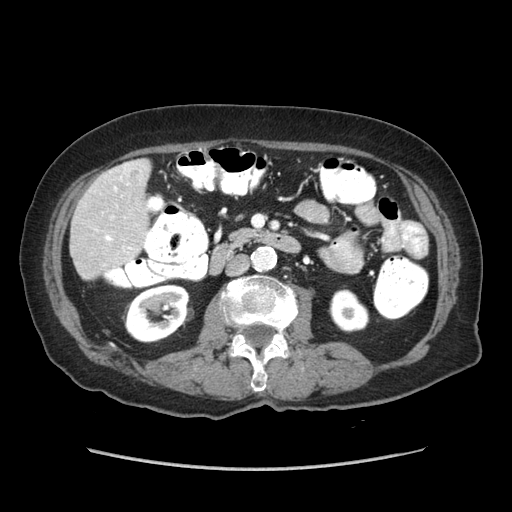
Contrast-enhanced abdominal CT (liver protocol), one axial slice; position 18 of 89 along the scan axis; reconstruction kernel STANDARD; soft-tissue window (W 400 / L 40 HU); 2.5 mm slice thickness; 512 × 512 image matrix, field of view 360 × 360 mm. From the clinical record (not read from this slice): diagnosis: hepatocellular carcinoma (patient treated with transarterial chemoembolisation; whether this scan precedes or follows treatment is not stated here); TNM stage (as recorded): Stage-IIIA; Child-Pugh class: A; tumour differentiation: well differentiated; tumour nodularity: multinodular.
Annotated regions visible in this slice (semi-automatic segmentation, software-assisted and operator-edited):
- liver parenchyma outside the tumour (the mass and vessels are separate outlines, so this box may not span the whole liver): bounding box [x1, y1, x2, y2] px = [70, 158, 150, 278]
- liver vessels: [105, 168, 133, 250]